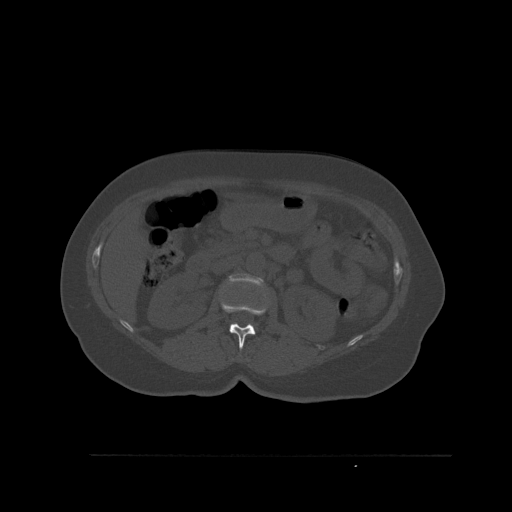
CT including the spine, one axial slice; position 260 of 527 along the scan axis; bone window (W 1800 / L 400 HU); 1.5 mm slice thickness; 512 × 512 image matrix. Female patient, age 73 years. Case-level facts recorded for this patient, not image findings: primary cancer: breast.
Annotated regions visible in this slice (semi-automatically segmented with operator editing):
- L1 vertebra: box from (x=221, y=302) to (x=267, y=350) px
- L2 vertebra: (x=229, y=273)–(x=262, y=285)